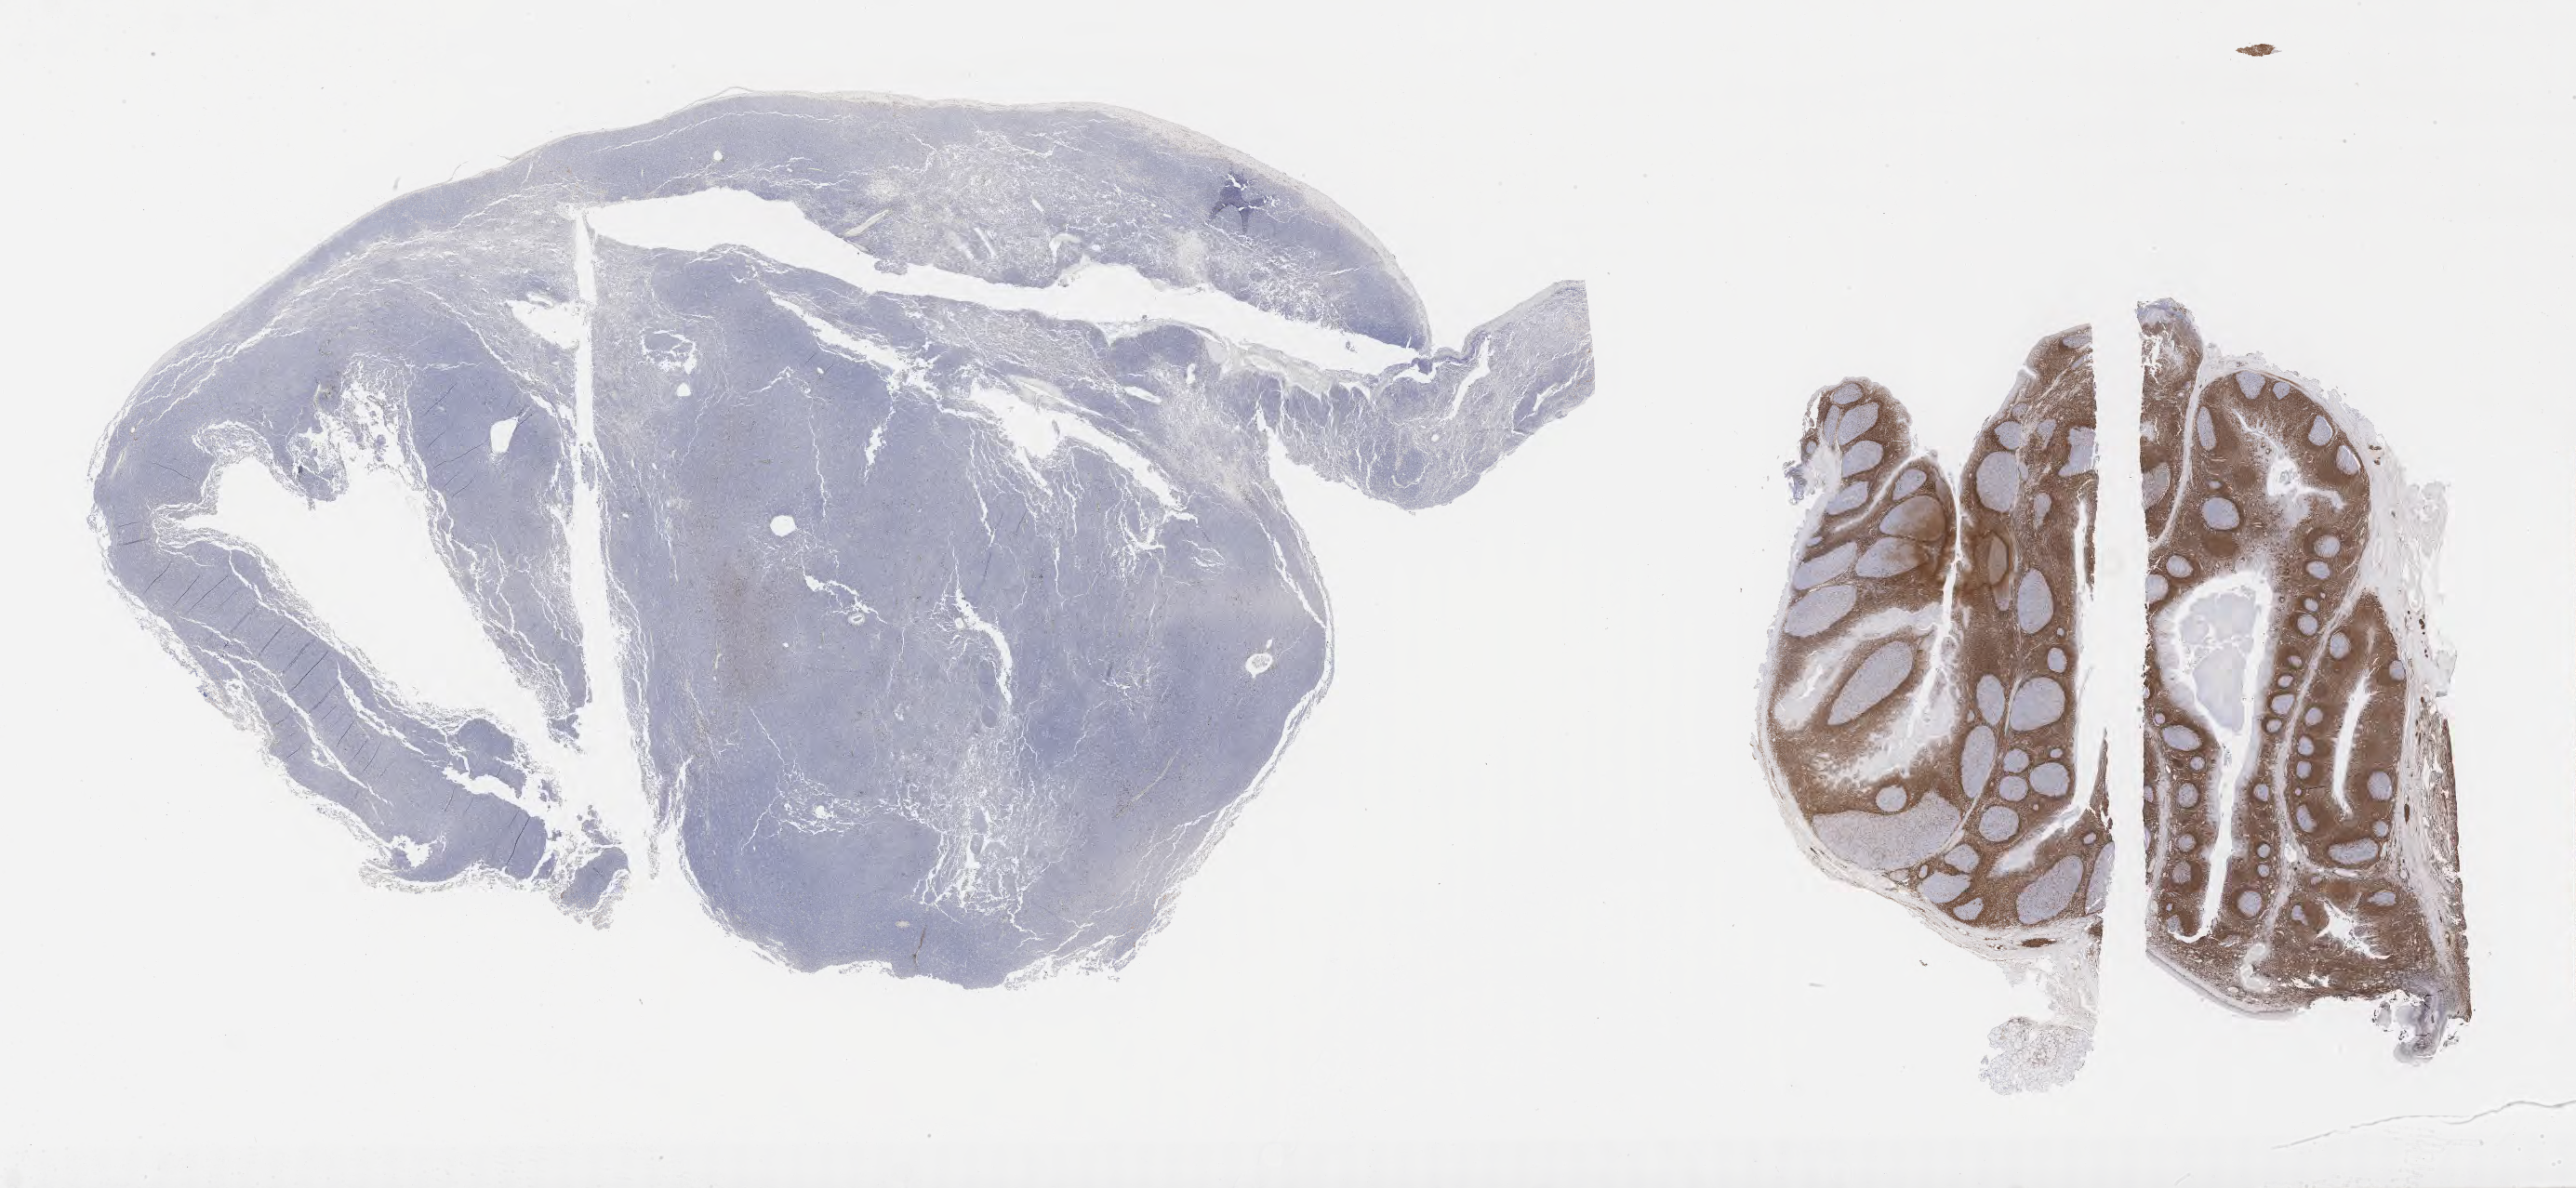
Whole-slide image, immunohistochemical stain for BCL2, whole scanned area (about 44.8 x 20.7 mm) shown as a low-resolution overview. Tumor tissue. Female patient; age at initial diagnosis 3 years.
Diagnosis: Burkitt lymphoma, NOS.